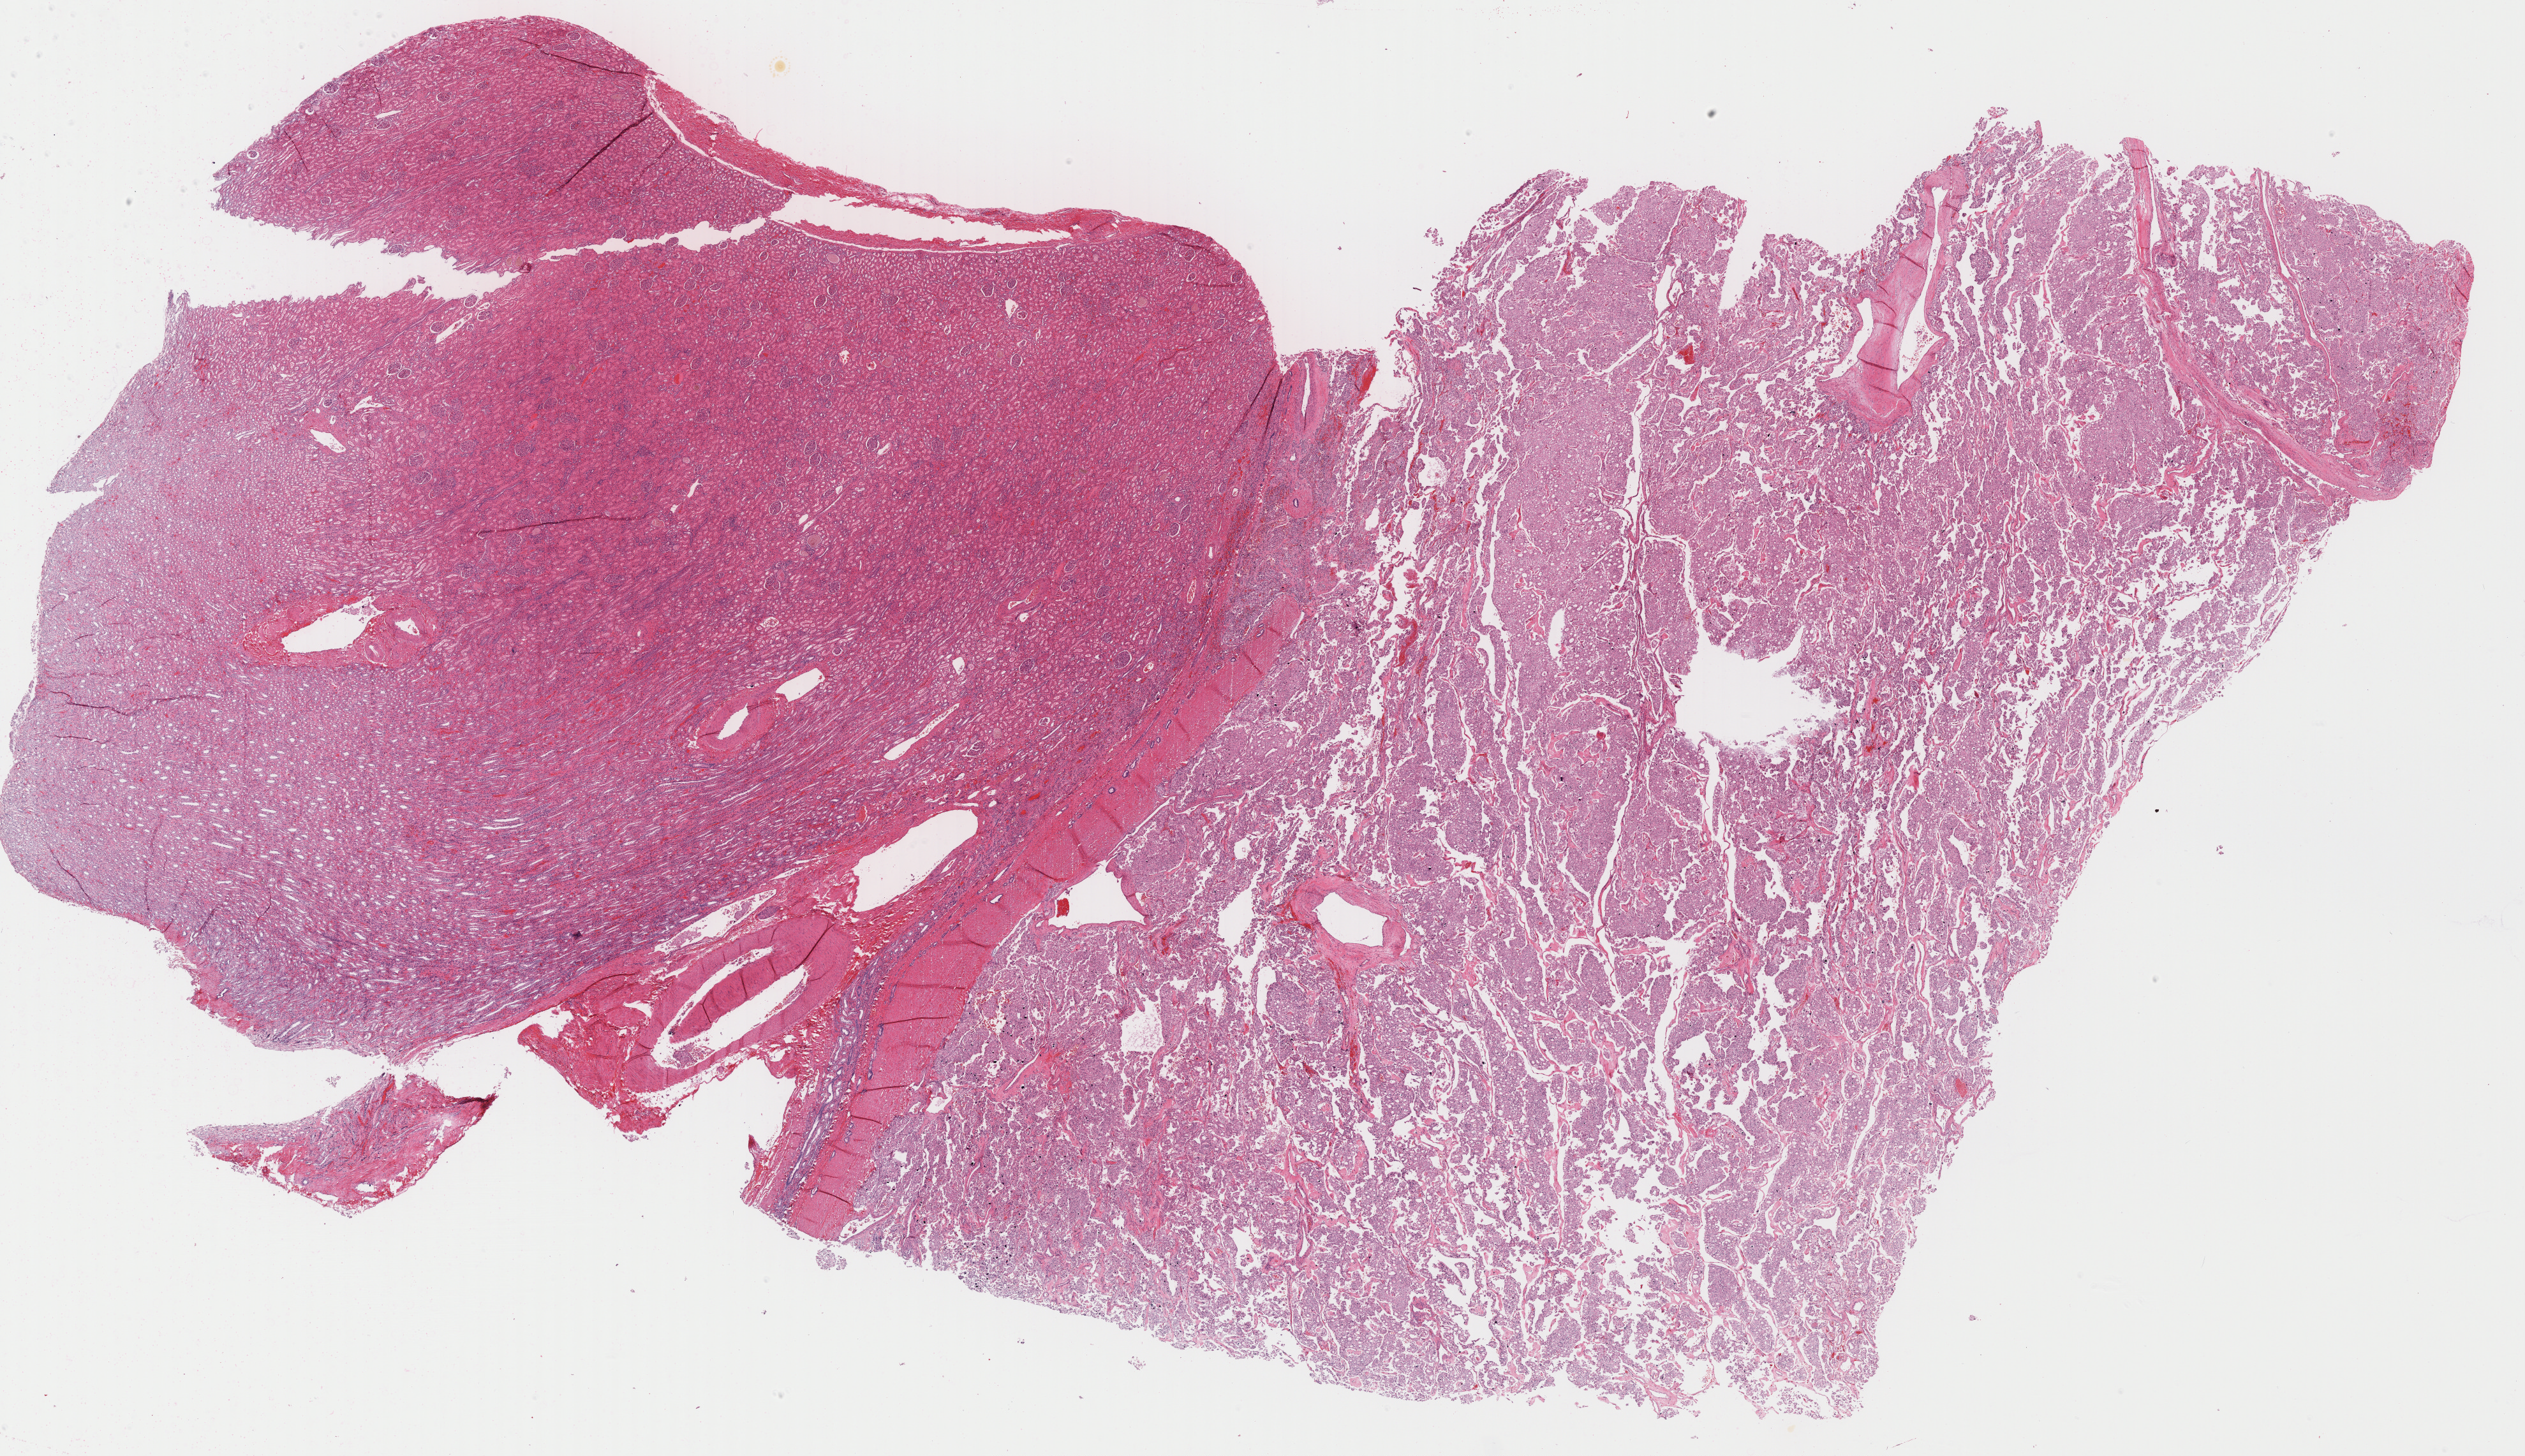
Whole-slide histology image, Hematoxylin and eosin (H&E) stained, low-resolution overview of the scanned area, about 31.9 x 18.4 mm, FFPE section, sample: primary tumour, kidney. Female, age 38 years at initial diagnosis.
Laterality: right. AJCC pathologic stage: III (6th edition). Diagnosis: Renal cell carcinoma, chromophobe type.